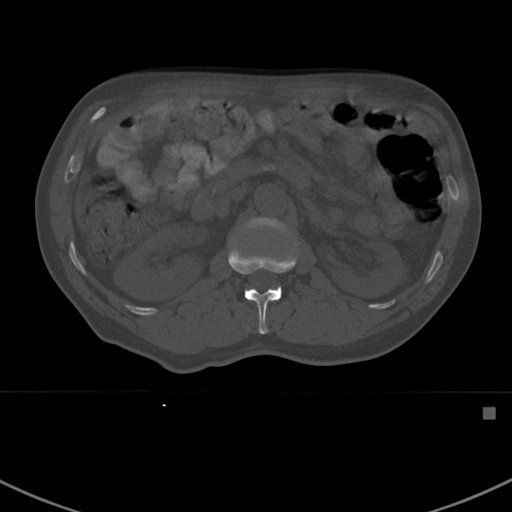
CT including the spine, one axial slice; slice 303 of 412 in the series (ordered by position); reconstruction kernel Br40s; bone window (W 1800 / L 400 HU); 1.5 mm slice thickness; 512 × 512 image matrix, field of view 358 × 358 mm. Patient: male, 59 years. Case-level facts recorded for this patient, not image findings: primary cancer: prostate.
Annotated regions visible in this slice (semi-automatic segmentation, software-assisted and operator-edited):
- L1 vertebra: bounding box <228,242,297,334> (left, top, right, bottom; pixels)
- L2 vertebra: <240,217,290,234>